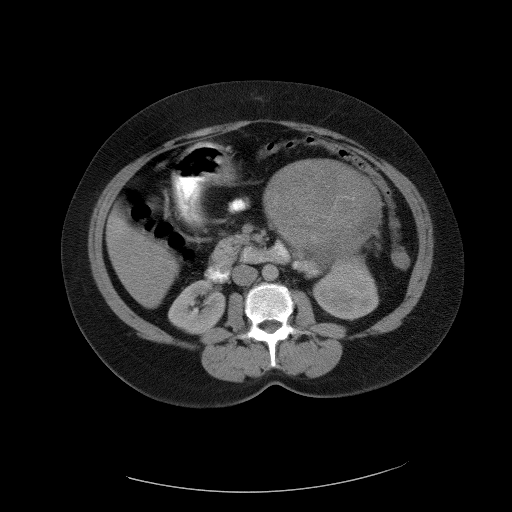
Contrast-enhanced abdominal CT, one axial slice; intravenous contrast given; soft-tissue window (W 400 / L 40 HU); 5 mm slice thickness; 512 × 512 image matrix. Patient: female, 55 years. From the clinical record (not read from this slice): diagnosis: adrenocortical carcinoma; tumour side: left adrenal; tumour size at pathology: 22 cm; Ki-67 index: 10 %.
Structures marked on this image (semi-automatically segmented with operator editing):
- mass: box from (x=267, y=161) to (x=378, y=258) px